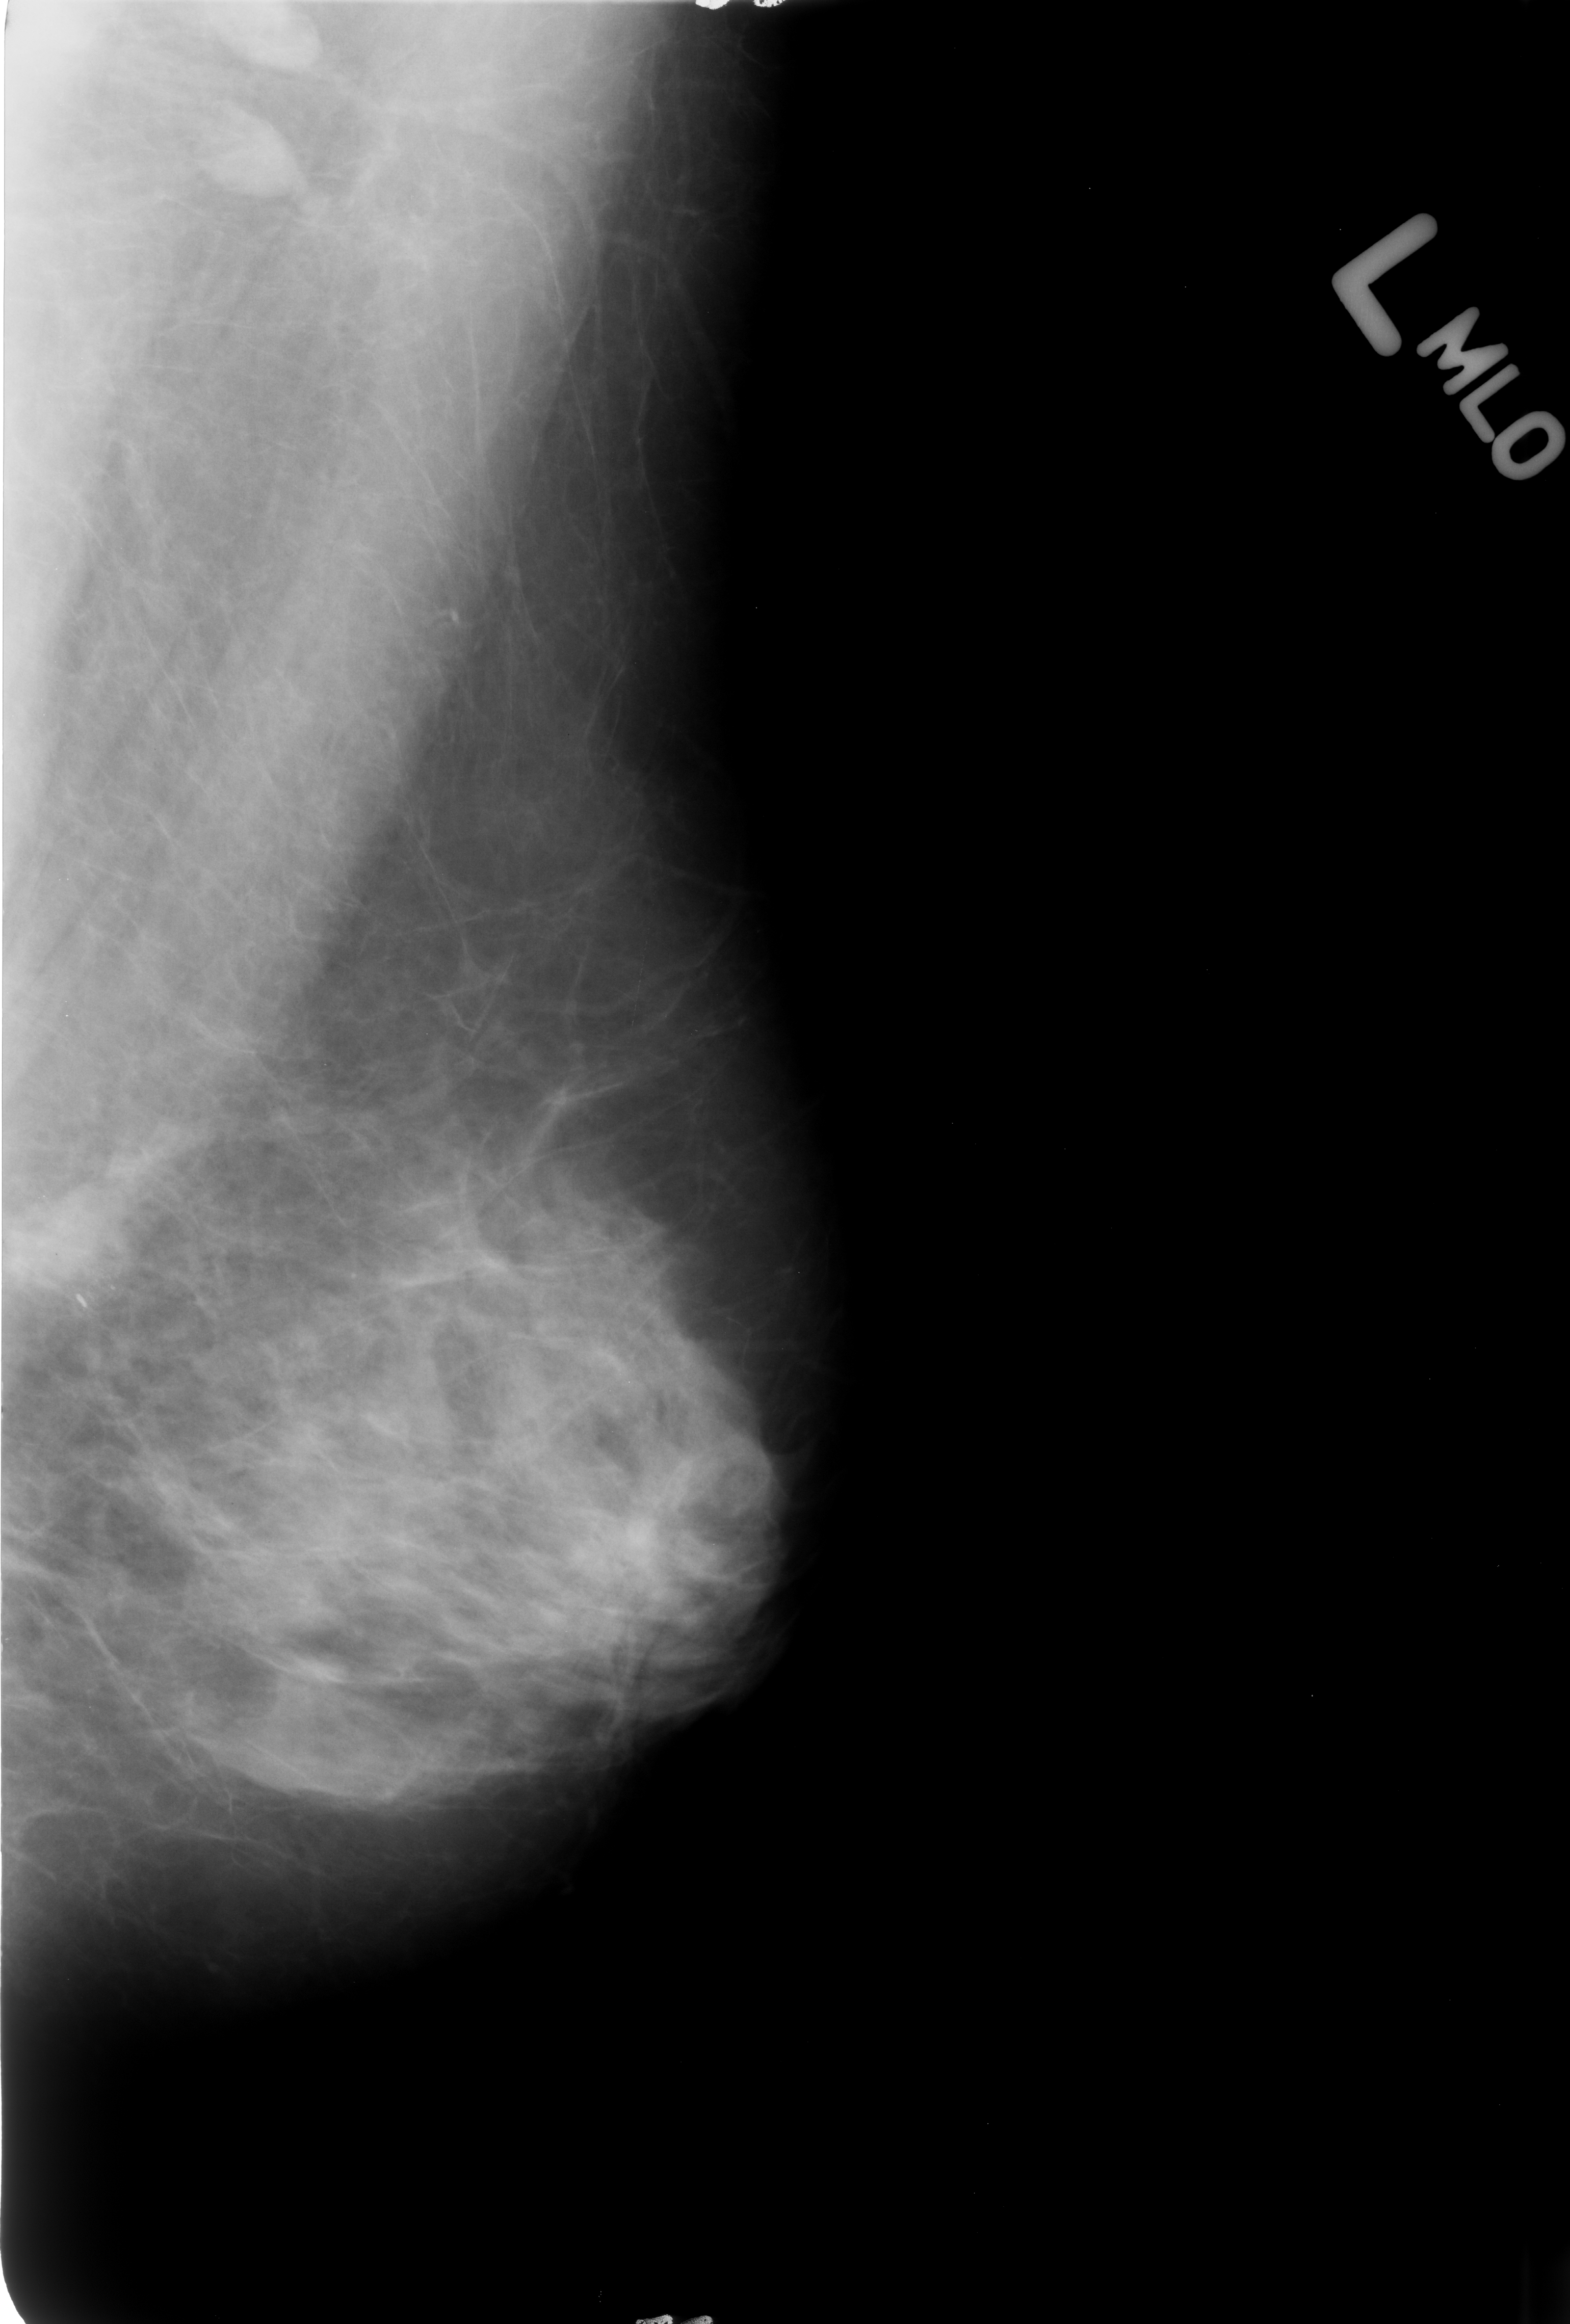
Mammogram (digitized film); left breast; mediolateral oblique (MLO) view; breast composition: heterogeneously dense (BI-RADS density category 3 of 4).
Finding: calcifications, morphology pleomorphic, distribution clustered; BI-RADS assessment category 4; pathology result (as recorded, not read from the image): malignant.